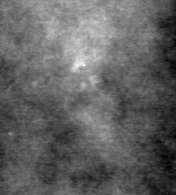
Region of interest cut from a scanned film mammogram (one marked finding); right breast; MLO view; BI-RADS breast density category 3 (scale 1–4).
- Finding: calcifications, morphology pleomorphic, distribution clustered; BI-RADS assessment category 4; subtlety rating 3 on a 1 (subtle) to 5 (obvious) scale; pathology result (as recorded, not read from the image): benign.